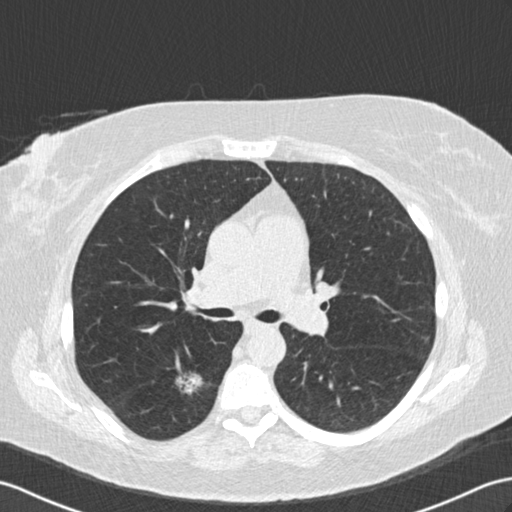
Axial slice from a low-dose chest CT screening exam. Second screening round (one year after baseline). Lung window (W 1500 / L -600 HU). Female, age 65 years at enrolment. Former smoker at enrolment.
- Expert reader's lesion annotation, box from (x=157, y=356) to (x=214, y=413) px.
- Reader record for this screening exam (exam-level; its link to the box is not recorded): non-calcified nodule or mass ≥4 mm, right lower lobe, 18 × 16 mm, spiculated (stellate) margins, soft tissue attenuation, pre-existing on the prior screen: yes; interval growth: yes.
- Participant outcome: lung cancer diagnosed 239 days after this screen — adenocarcinoma, NOS, right lower lobe, moderately differentiated (G2), stage IA (AJCC 6th edition), 25 mm at pathology.